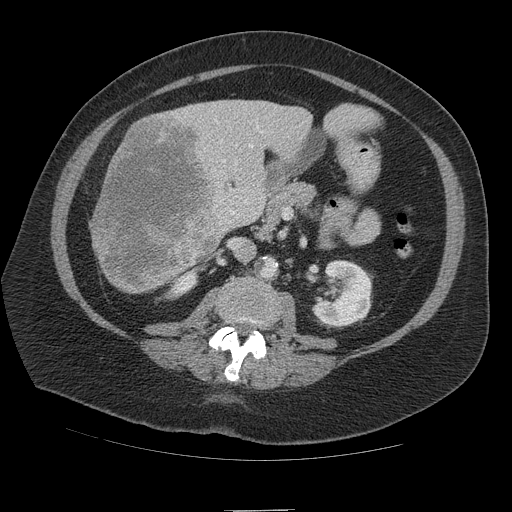
Contrast-enhanced abdominal CT (liver protocol), one axial slice. Position 43 of 109 along the scan axis. Reconstruction kernel STANDARD. 140 kVp. Soft-tissue window (W 400 / L 40 HU). 2.5 mm slice thickness. 512 × 512 image matrix, field of view 420 × 420 mm. From the clinical record (not read from this slice): diagnosis: hepatocellular carcinoma (patient treated with transarterial chemoembolisation; whether this scan precedes or follows treatment is not stated here); TNM stage (as recorded): Stage-IVB; Child-Pugh class: A; tumour differentiation: poorly differentiated; tumour nodularity: multinodular.
Outlined on this slice (semi-automatically segmented with operator editing):
- liver parenchyma outside the tumour (the mass and vessels are separate outlines, so this box may not span the whole liver): bounding box [x1, y1, x2, y2] px = [92, 100, 378, 292]
- mass: [90, 114, 225, 293]
- liver vessels: [214, 119, 263, 222]